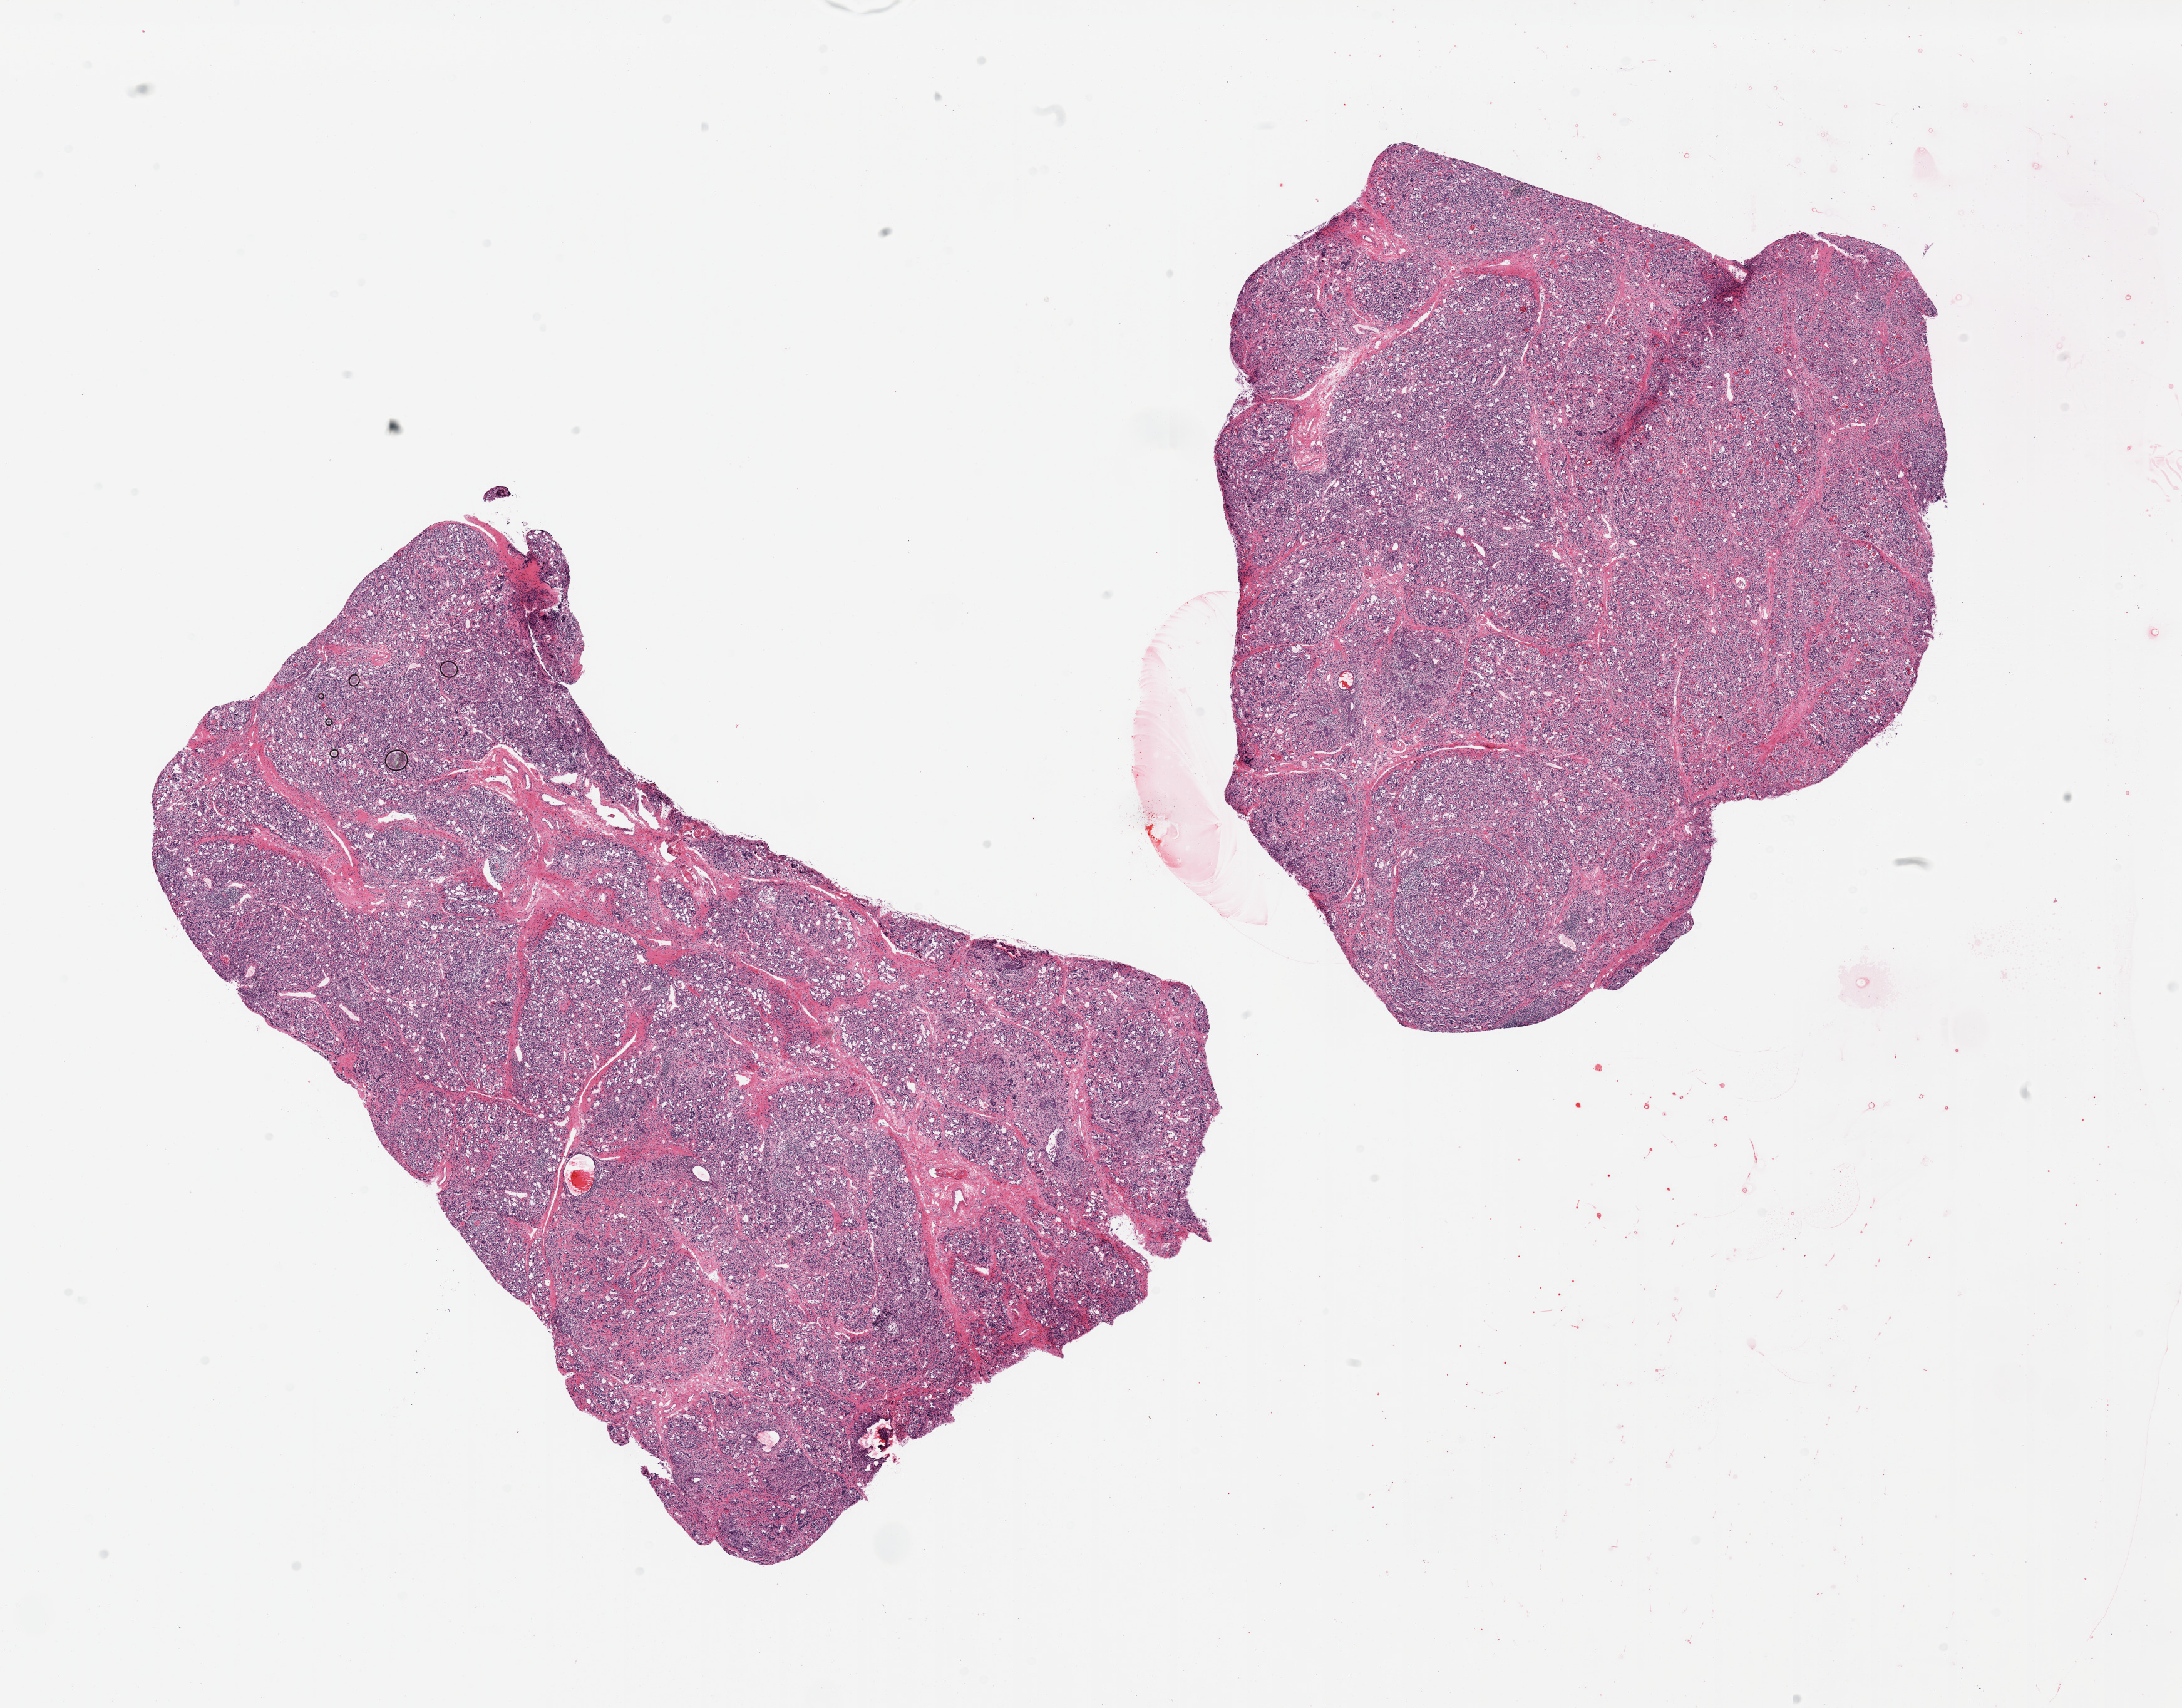
Digitized hematoxylin and eosin (H&E)-stained section — a low-resolution overview of the entire scanned area, about 27.6 x 21.6 mm. PAXgene-fixed paraffin-embedded (PFPE) section. Section of thyroid (target tissue). Tissue donor sample. Donor: male.
Reviewer comment on this tissue sample: 2 pieces, atrophy? infiltrative process, markedly autolyzed.